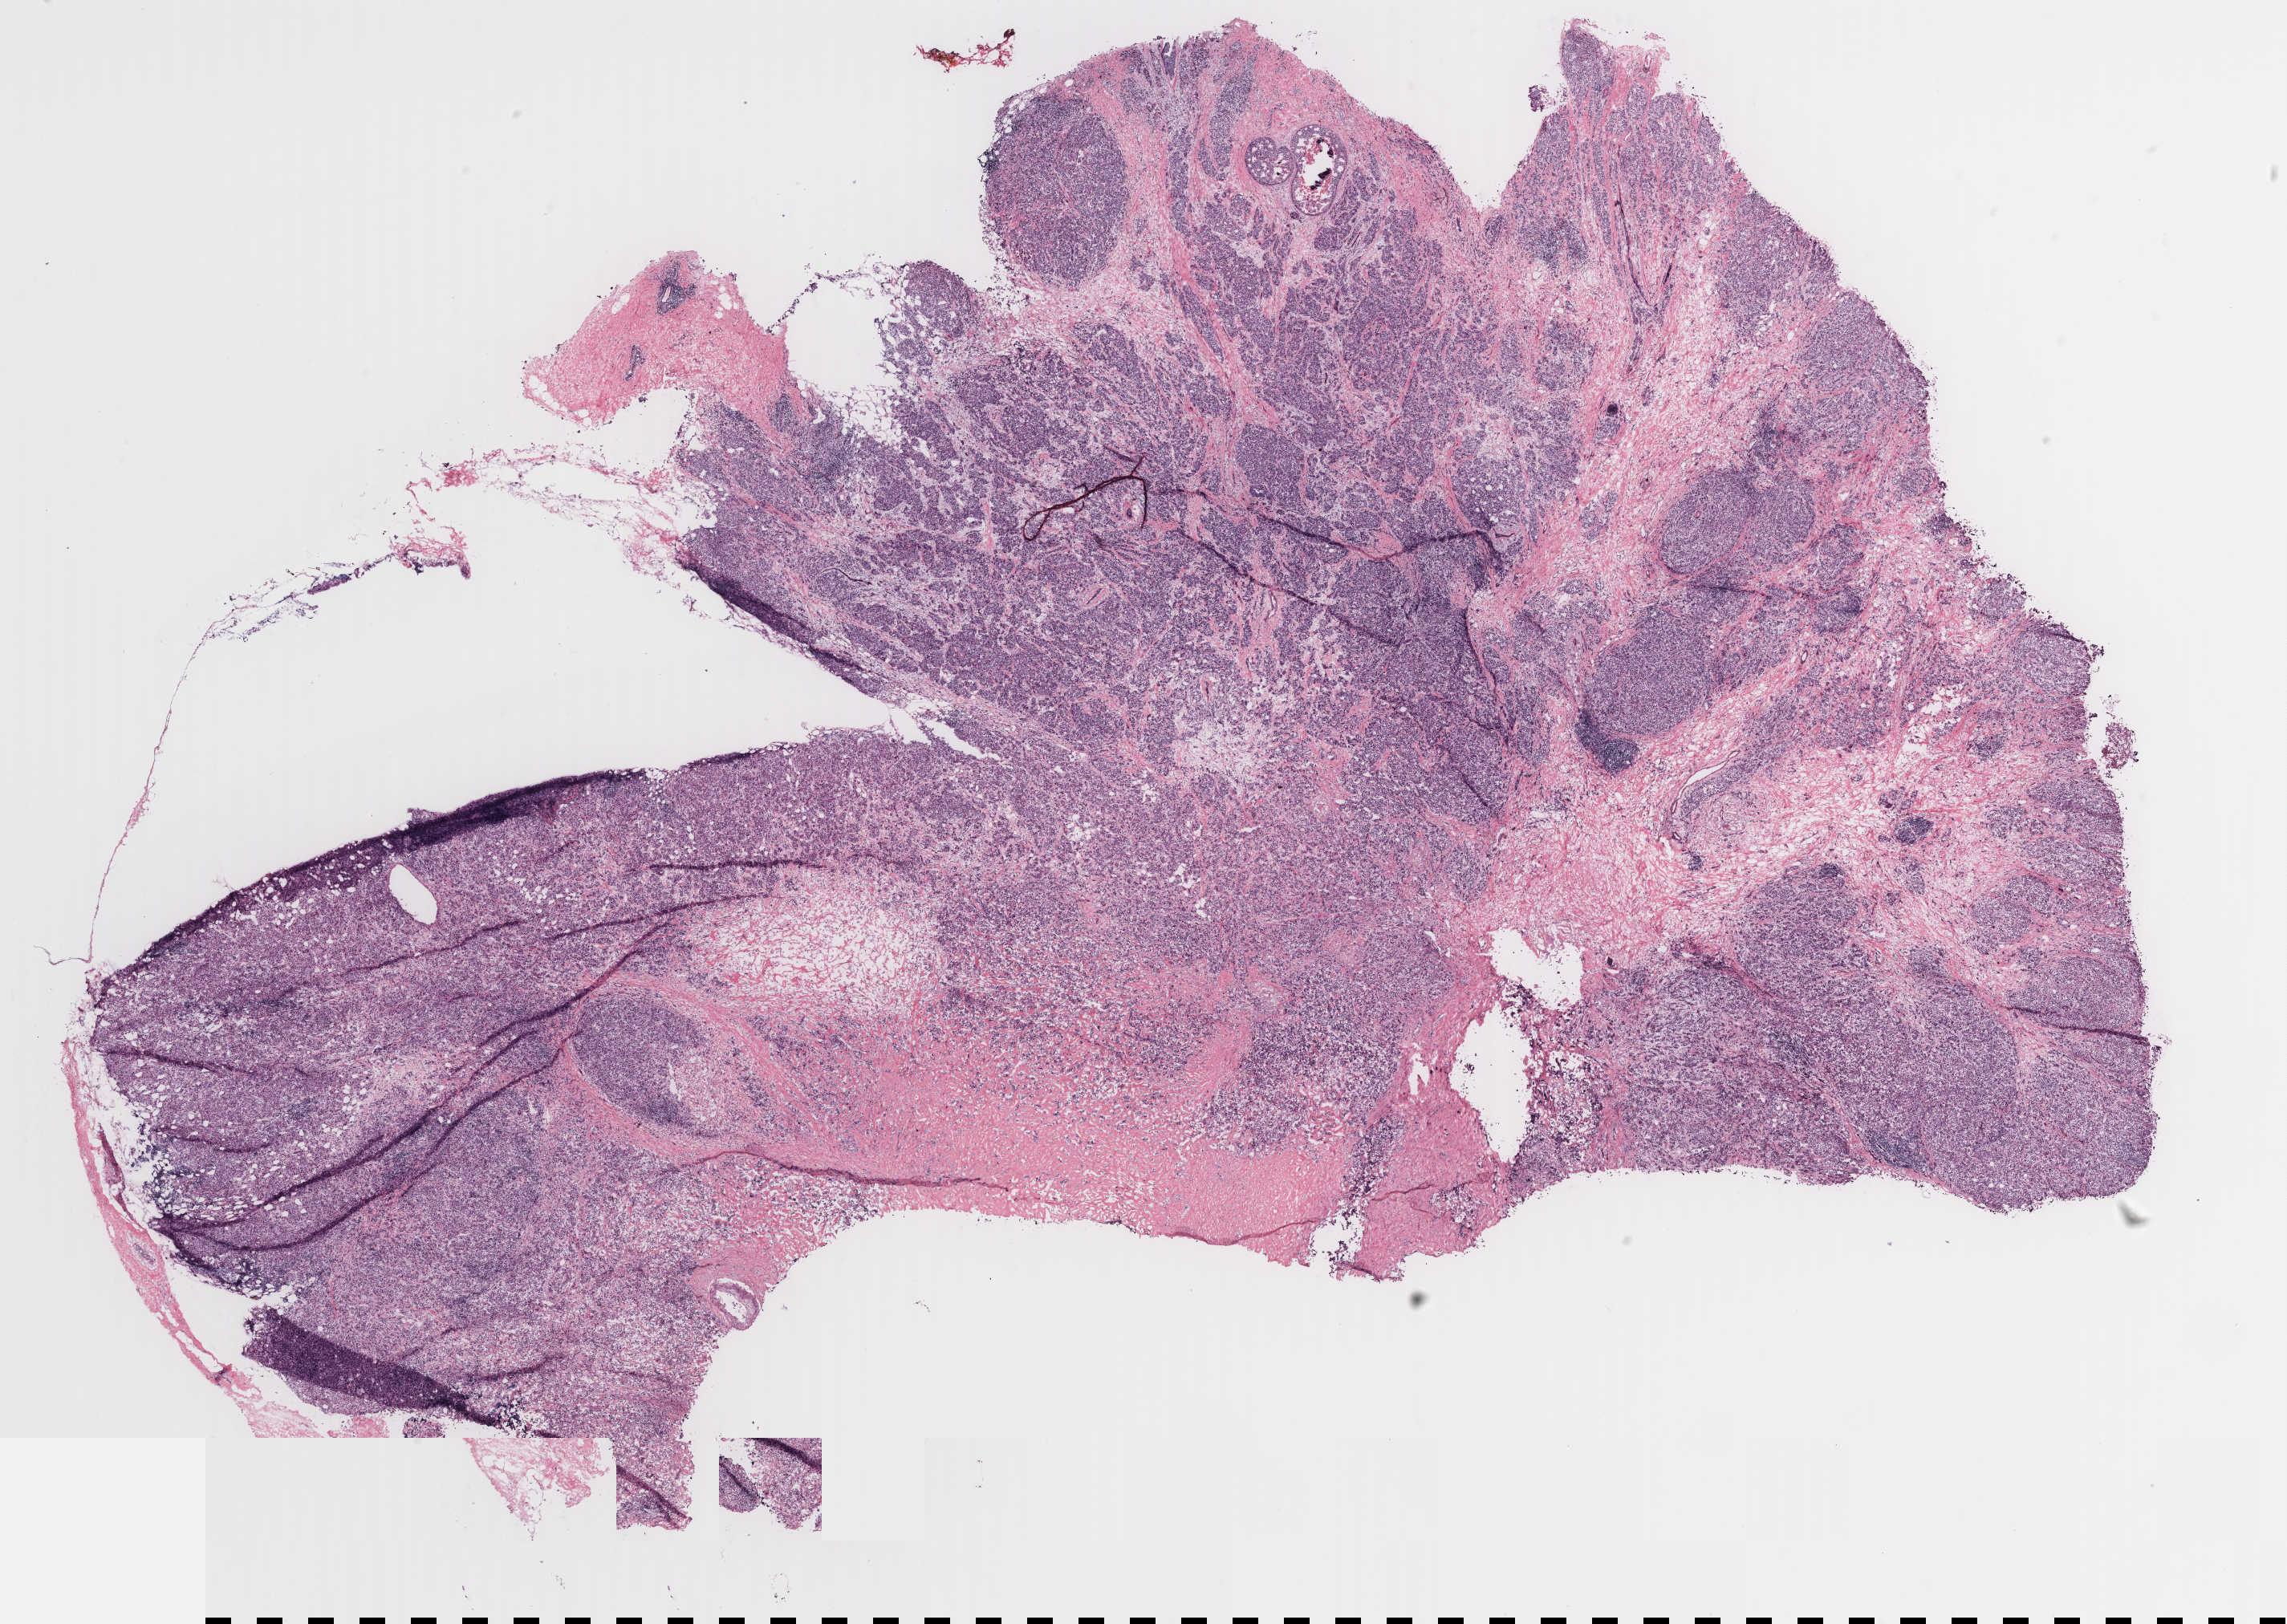
Digitized H&E tissue section (whole slide) — a low-resolution overview of the entire scanned area, about 22.8 x 16.2 mm (slide scanned at 40x). Breast, tissue type not recorded. 65-year-old female patient.
Patient diagnosis: Infiltrating lobular carcinoma, NOS.